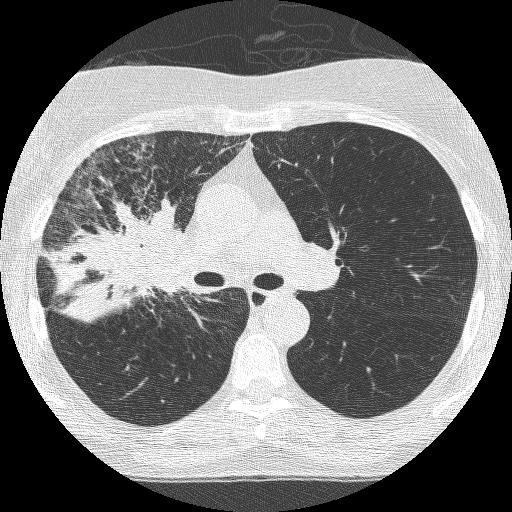
Low-dose screening chest CT, axial slice; third annual screen; lung window (W 1500 / L -600 HU); 1.25 mm slice thickness; lung (sharp) reconstruction kernel (BONE). Female participant, aged 64 years at enrolment.
Expert-annotated lung lesion, box from (x=79, y=203) to (x=203, y=328) px. Screening reader's record for this exam (one nodule recorded; not confirmed to be the boxed lesion): non-calcified nodule or mass ≥4 mm, right upper lobe, 49 × 43 mm, spiculated (stellate) margins, soft tissue attenuation, pre-existing on the prior screen: yes; interval growth: yes. Participant outcome: lung cancer diagnosed 7 days after this screen — adenocarcinoma, NOS, right upper lobe, right middle lobe, right hilum, stage IV (AJCC 6th edition), 85 mm at pathology.